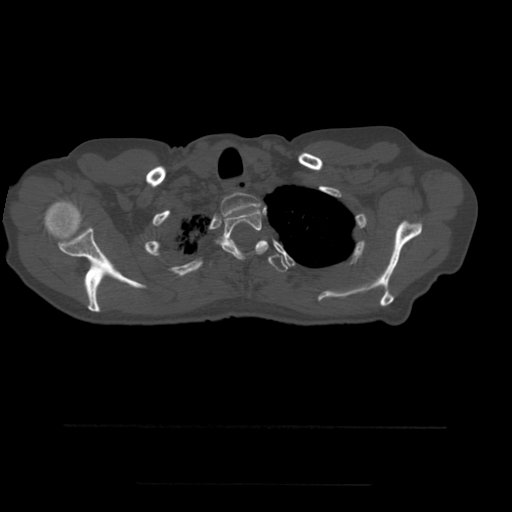
CT including the spine, one axial slice. Position 432 of 544 along the scan axis. Bone window (W 1800 / L 400 HU). 512 × 512 image matrix, field of view 350 × 350 mm. Patient age 58 years. From the clinical record (not read from this slice): primary cancer: lung.
Annotated regions visible in this slice (semi-automatic segmentation, software-assisted and operator-edited):
- T1 vertebra: box from (x=221, y=193) to (x=262, y=216) px
- T2 vertebra: (x=218, y=207)–(x=268, y=259)
- T3 vertebra: (x=235, y=241)–(x=288, y=274)